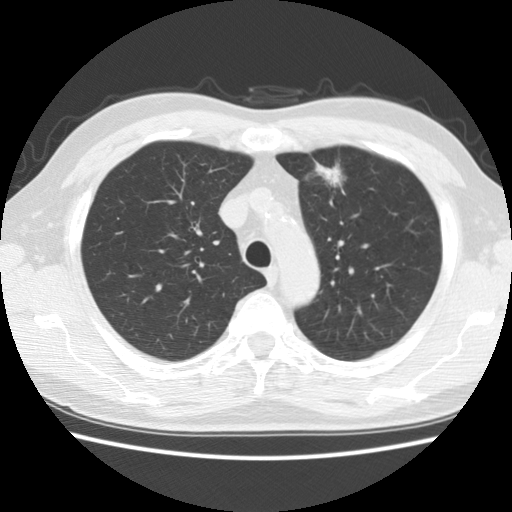
Axial slice from a low-dose chest CT screening exam, second screening round (one year after baseline), lung window (W 1500 / L -600 HU), 2.5 mm slice thickness, standard (soft-tissue) reconstruction kernel (STANDARD). Male, age 63 years at enrolment.
Expert reader's lesion annotation, bounding box [x1, y1, x2, y2] px = [298, 147, 357, 202]. Screening reader's record for this exam (one nodule recorded; not confirmed to be the boxed lesion): non-calcified nodule or mass ≥4 mm, left upper lobe, 23 × 18 mm, spiculated (stellate) margins, soft tissue attenuation, pre-existing on the prior screen: yes; interval growth: yes. Lung cancer was diagnosed 83 days after this screen: adenocarcinoma, NOS, left upper lobe, moderately differentiated (G2), stage IA (AJCC 6th edition), 14 mm at pathology.